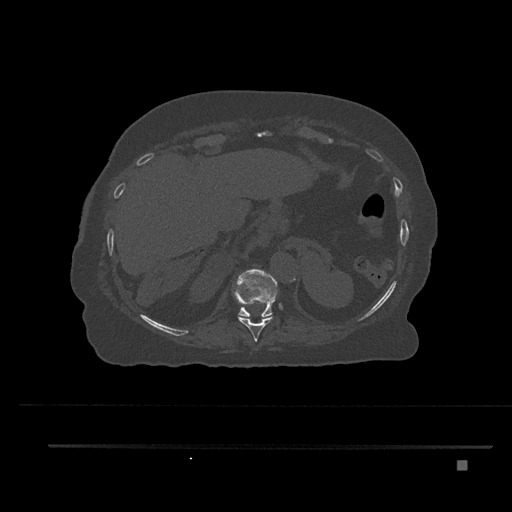
CT including the spine, one axial slice; slice 337 of 797 in the series (ordered by position); bone window (W 1800 / L 400 HU); 512 × 512 image matrix. Female patient, age 76 years. From the clinical record (not read from this slice): primary cancer: lung.
Outlined on this slice (semi-automatically segmented with operator editing):
- T10 vertebra: box from (x=233, y=286) to (x=274, y=341) px
- T11 vertebra: (x=237, y=269)–(x=278, y=317)